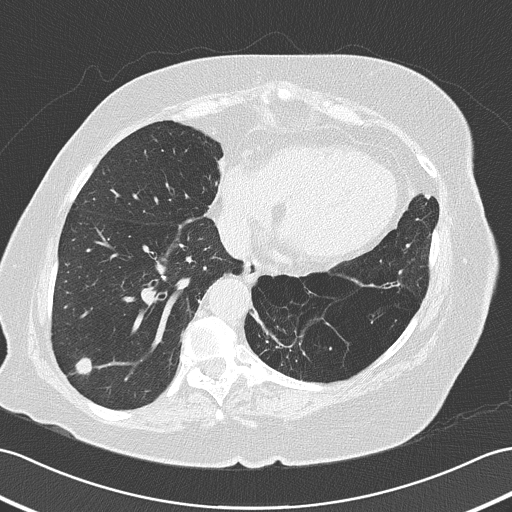
Chest CT (low-dose screening protocol), one axial image; baseline screening round; lung window (W 1500 / L -600 HU); lung (sharp) reconstruction kernel (B50f); slice 102 of 161 in the series; 512 × 512 image matrix, field of view 353 × 353 mm. Female, age 73 years at enrolment. Former smoker at enrolment.
Lesion marked by an expert reader, bounding box (x1, y1, x2, y2) in pixels: (54, 337, 101, 385). The screening reader recorded 4 non-calcified nodules or masses ≥4 mm on this exam (right lower lobe, right upper lobe, left upper lobe, left lower lobe); which of them this box marks is not recorded. Official screen result: positive, change unspecified: nodule(s) >= 4 mm or enlarging nodule(s), mass(es), or other non-specific abnormalities suspicious for lung cancer. Participant outcome: lung cancer diagnosed 50 days after this screen — adenocarcinoma, NOS, right lower lobe, poorly differentiated (G3), stage IB (AJCC 6th edition), 17 mm at pathology.